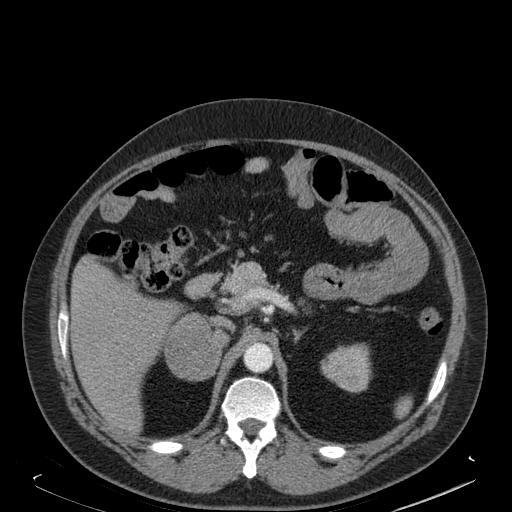
Contrast-enhanced abdominal CT, one axial slice. Slice 113 of 181 in the series (ordered by position). Soft-tissue window (W 400 / L 40 HU). 512 × 512 image matrix, field of view 405 × 405 mm. Male patient. From the clinical record (not read from this slice): diagnosis: adrenocortical carcinoma; tumour side: right adrenal; tumour size at pathology: 7.5 cm; Ki-67 index: 25 %.
Annotated regions visible in this slice (semi-automatic segmentation, software-assisted and operator-edited):
- mass: box from (x=165, y=313) to (x=218, y=380) px